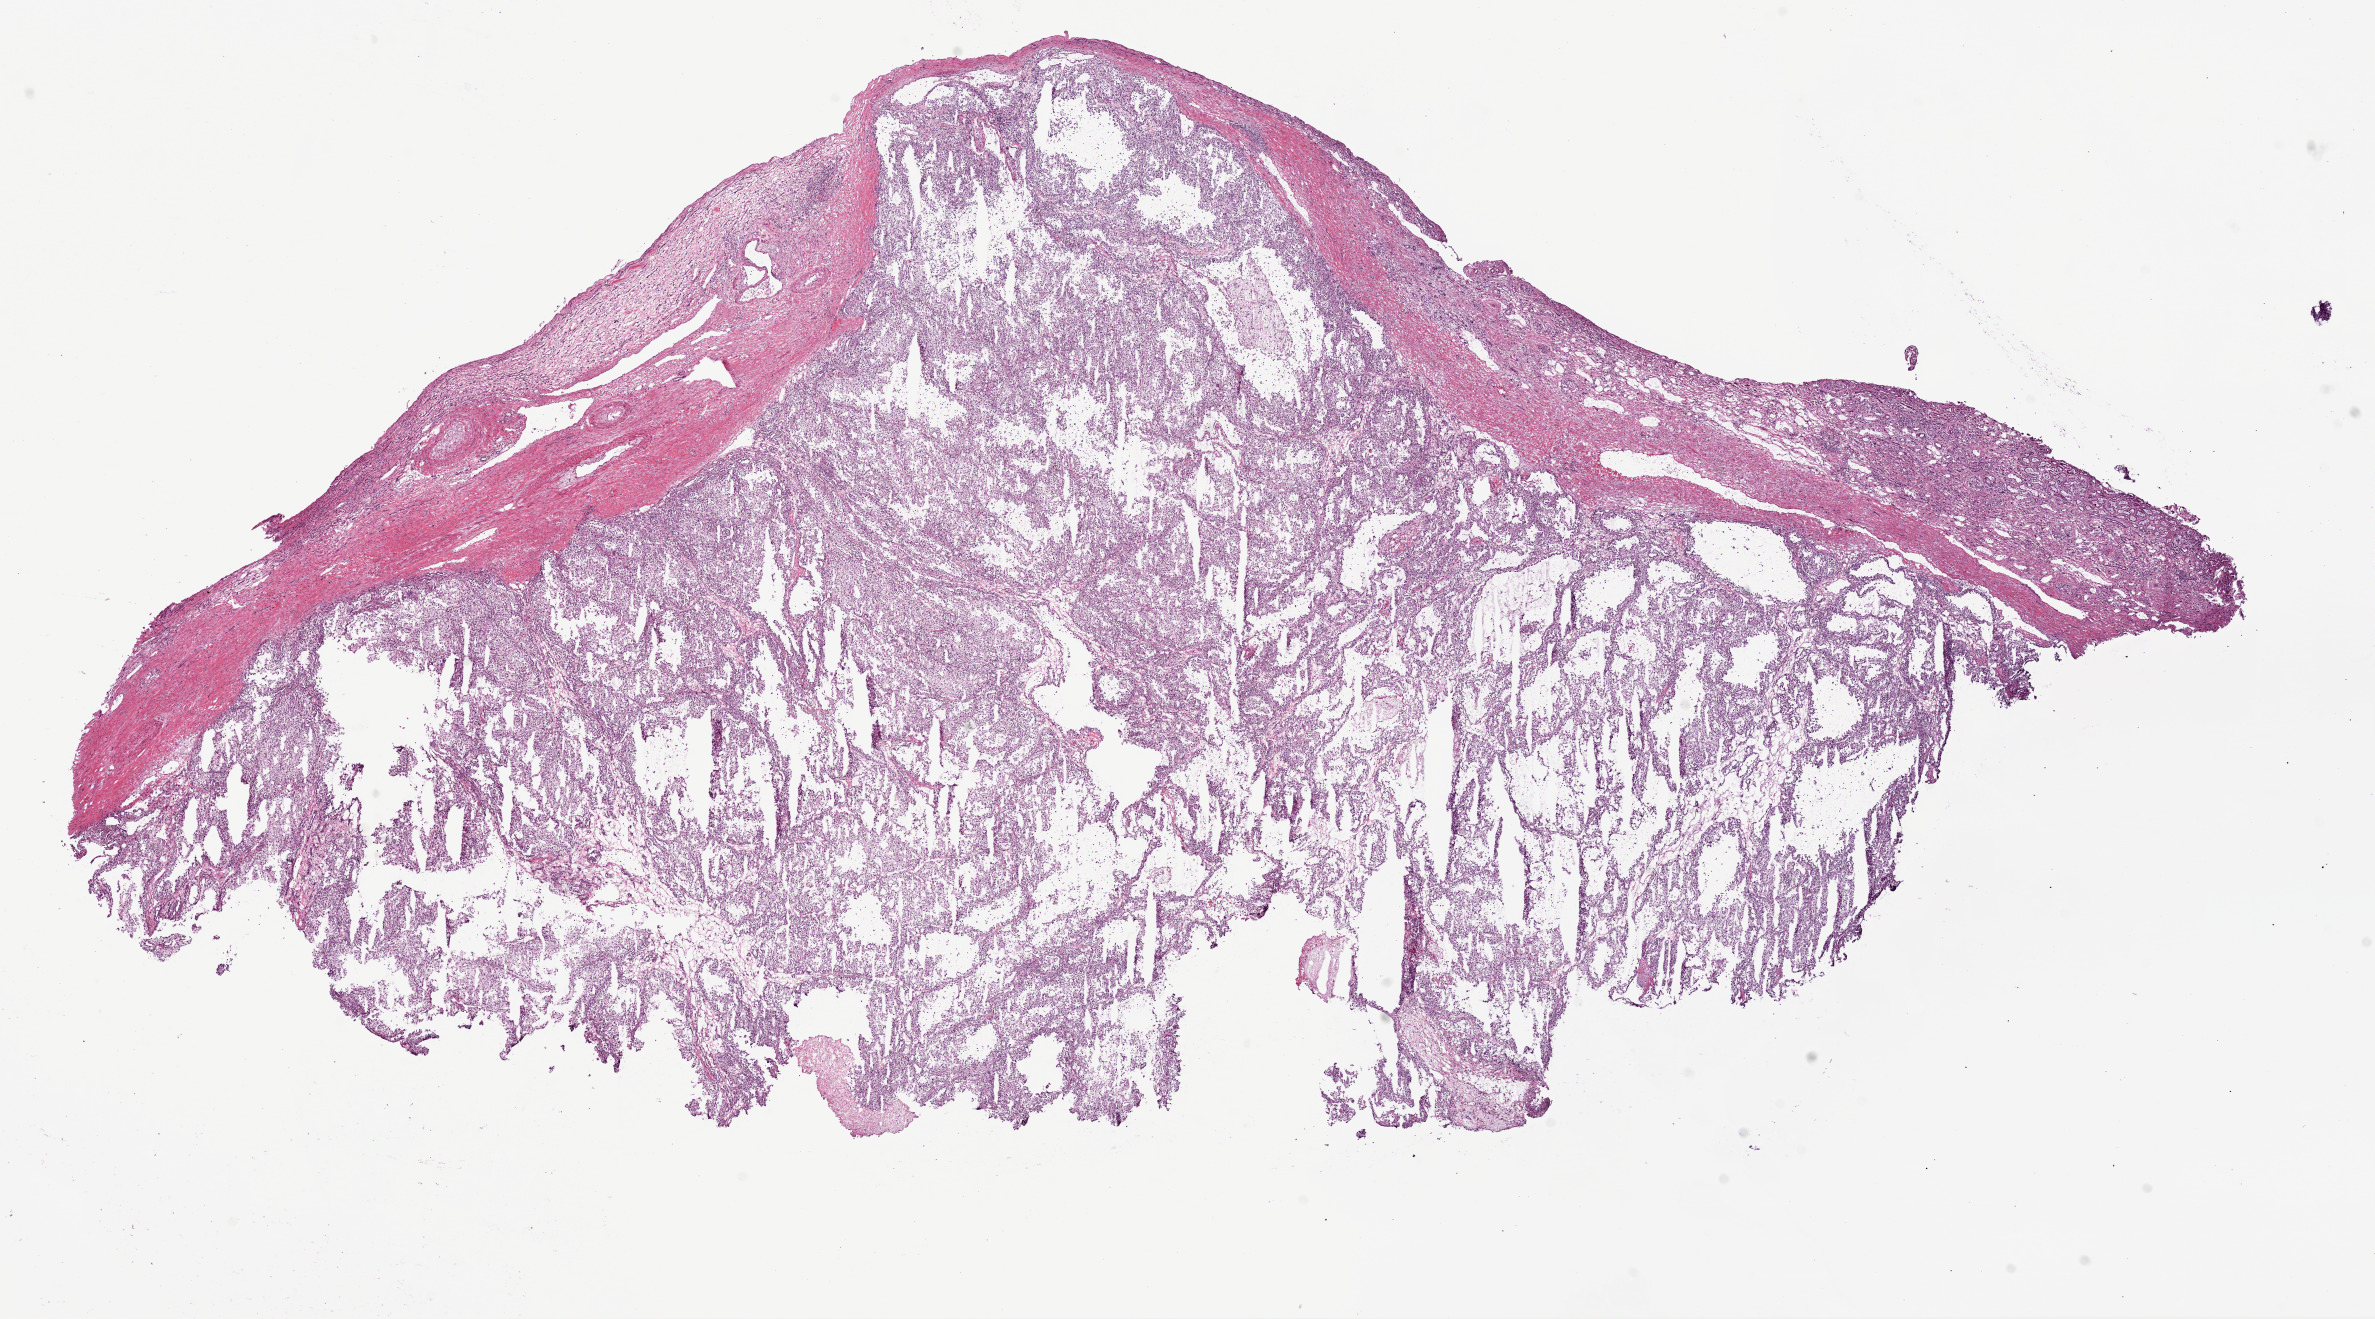
Digitized H&E tissue section (whole slide) — shown as a low-resolution overview of the whole scanned area (about 19.1 x 10.6 mm, acquisition: 20x scan), frozen section from the bottom of the tissue portion, kidney, primary tumour sample. Male patient; age at initial diagnosis 41 years. Histologic grade: G2 (moderately differentiated). Composition of this section per pathologist review: tumour cells 80%, tumour nuclei 75%, normal cells 5%, stromal cells 15%, necrosis 0%.
AJCC pathologic stage: I. Pathologic diagnosis: Clear cell adenocarcinoma, NOS.